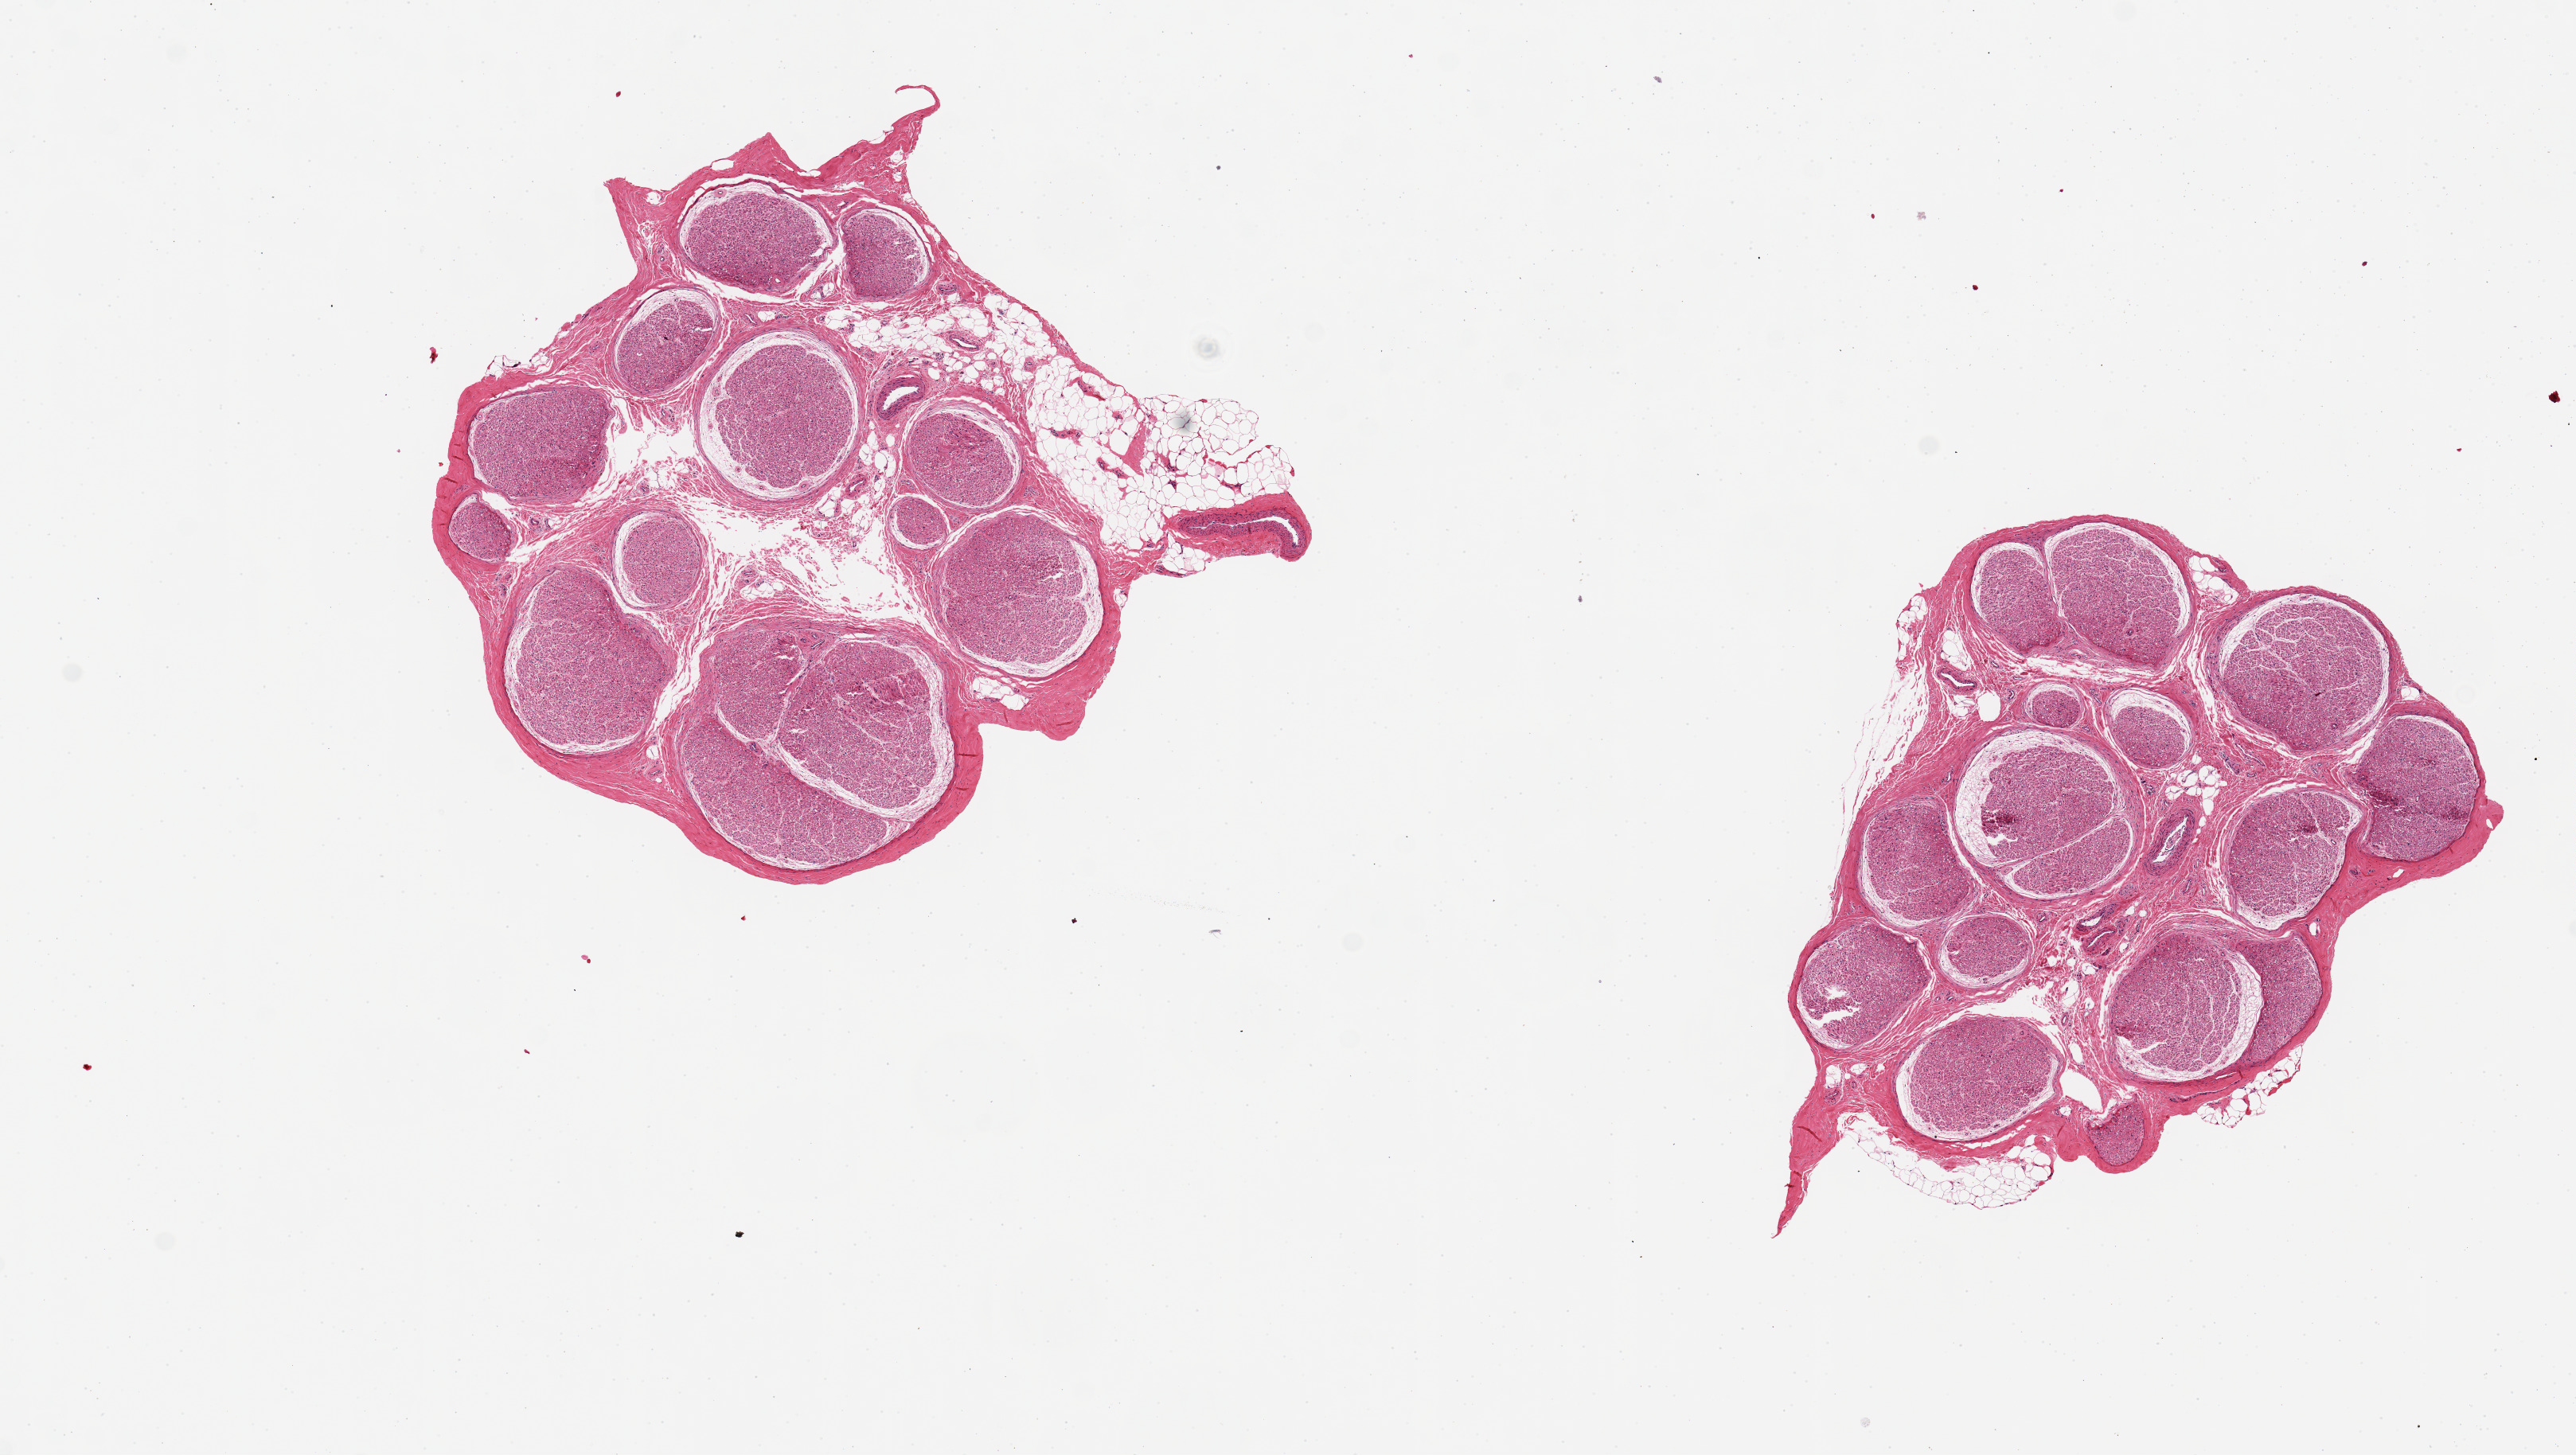
Digitized H&E-stained section, brightfield — whole scanned area (about 12.8 x 7.2 mm) shown as a low-resolution overview, PAXgene-fixed, paraffin-embedded tissue, sampled site (target tissue): tibial nerve, donor tissue sample. Male donor.
Review note (as recorded): 2 pieces, 4x4 & 3x3 mm; 10% peripheral fat in 1; <5% in other.